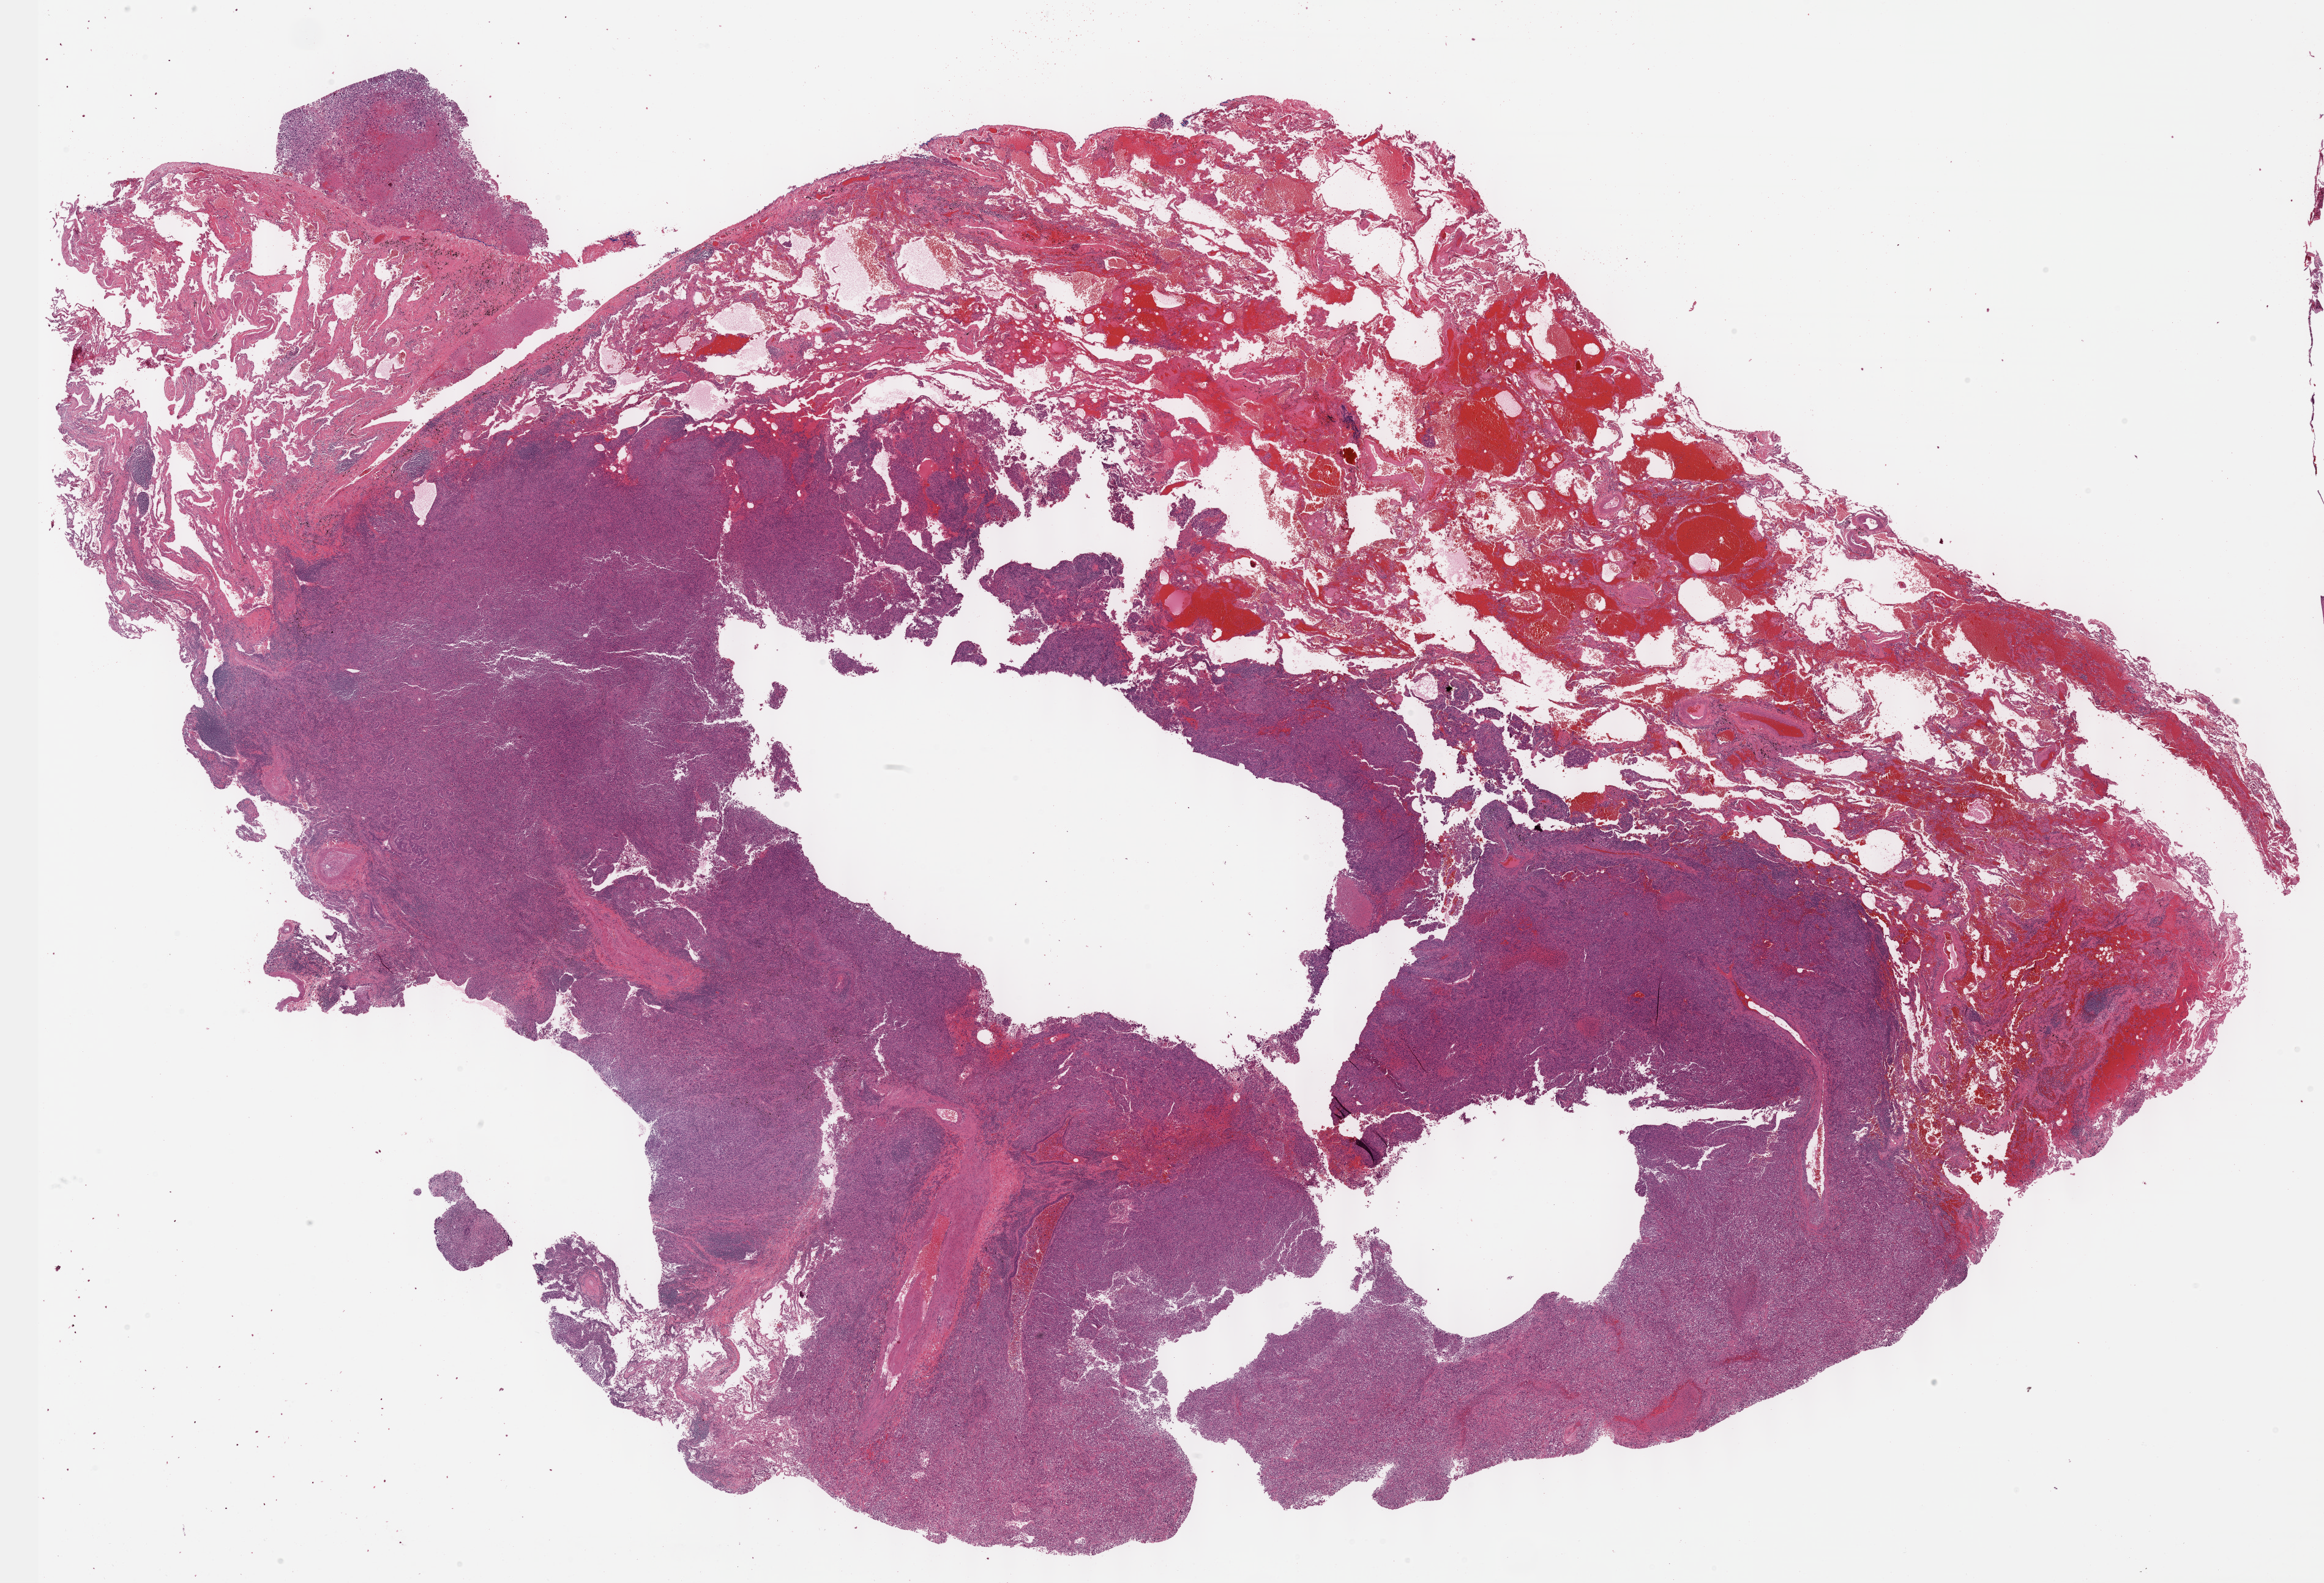
Digitized H&E tissue section (whole slide), whole scanned area (about 30.7 x 20.9 mm) shown as a low-resolution overview. Formalin-fixed paraffin-embedded (FFPE) diagnostic section. Lung, recurrent tumour sample. Male patient; age at initial diagnosis 72 years.
This section: recurrent tumour. Patient diagnosis: Adenocarcinoma with mixed subtypes (upper lobe, lung).